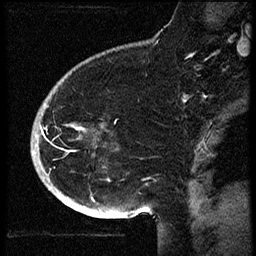
Breast MRI (dynamic contrast-enhanced), one sagittal slice. Slice 42 of 60 in the series (ordered by position). Dynamic contrast-enhanced study with each time point stored as its own series, time point 2 of 3 at this slice position (early post-contrast, ordered by acquisition time). 1.5 T. TE 4.2 ms, TR 18.9 ms. 2 mm slice thickness. 256 × 256 image matrix. Female patient. Case-level facts recorded for this patient, not image findings: setting: breast cancer imaged before/during neoadjuvant chemotherapy; receptor status: HR-positive, HER2-negative.
Annotated regions visible in this slice (semi-automatic segmentation, software-assisted and operator-edited):
- analysis volume of interest (the breast-tissue region the enhancement analysis was run in; not a lesion): bounding box [x1, y1, x2, y2] px = [34, 87, 108, 173]
- tumour enhancement mask (voxels above the 100 % enhancement threshold inside the analysis volume of interest): [35, 124, 72, 137]